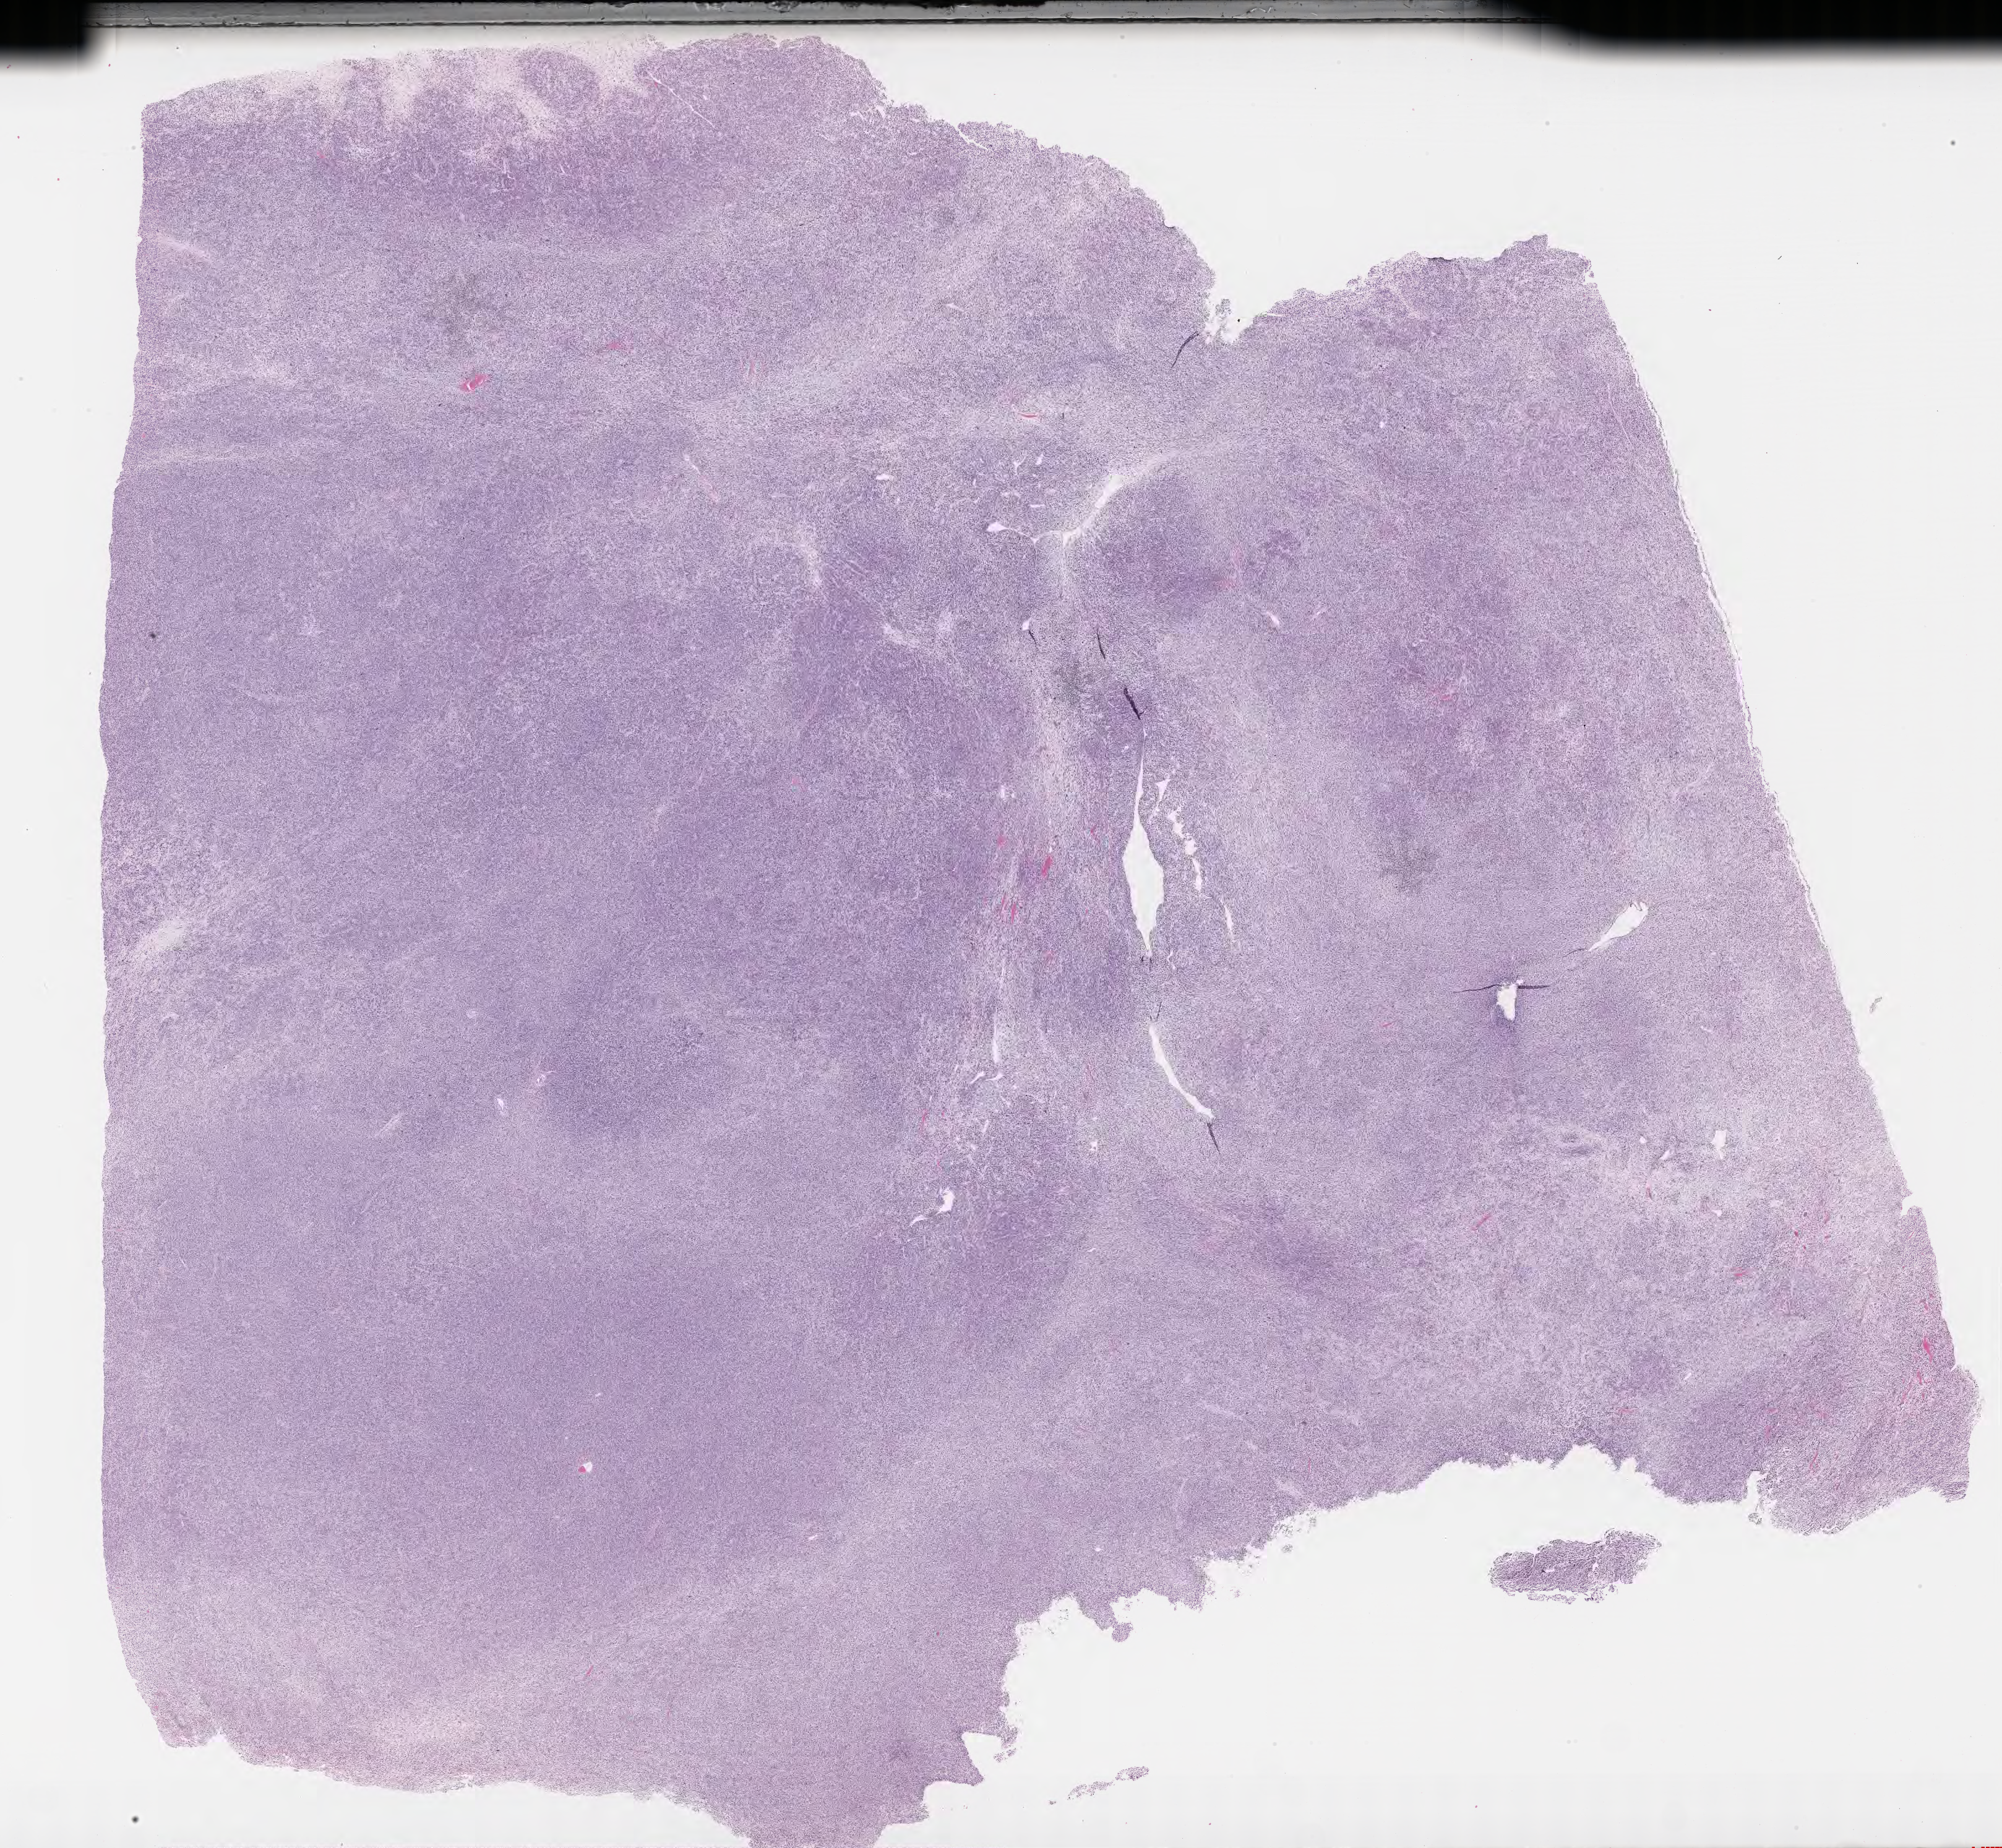
Haematoxylin and eosin whole-slide image of tumor tissue, low-resolution overview of the scanned area, about 26.2 x 24.2 mm; formalin-fixed, paraffin-embedded (FFPE) tissue; site: testicle-left. Patient: male, age 14.5 years at diagnosis.
• diagnosis: rhabdomyosarcoma; histological classification: embryonal rhabdomyosarcoma
• primary site (case record): testis-paratesticular
• metastatic status at presentation (as recorded): non-metastatic (unconfirmed)
• stage (as recorded): 1